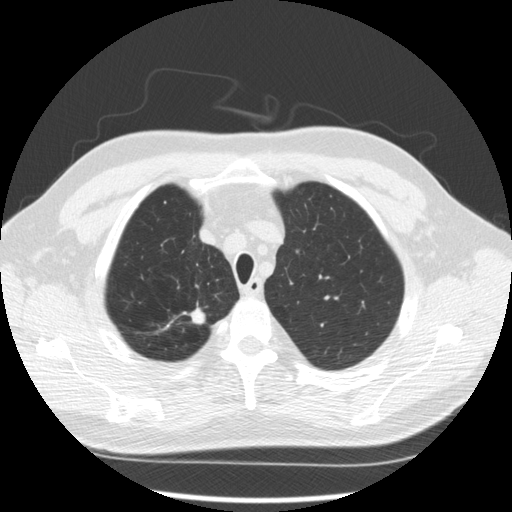
Axial slice from a low-dose chest CT screening exam. Second annual screen. Lung window (W 1500 / L -600 HU). 2.5 mm slice thickness. Male participant, aged 64 years at enrolment. Former smoker at enrolment.
- Lesion marked by an expert reader, bounding box (x1, y1, x2, y2) in pixels: (172, 299, 217, 334).
- The screening reader recorded 3 non-calcified nodules or masses ≥4 mm on this exam (right upper lobe, right upper lobe, right upper lobe); which of them this box marks is not recorded.
- Official screen result: positive, other.